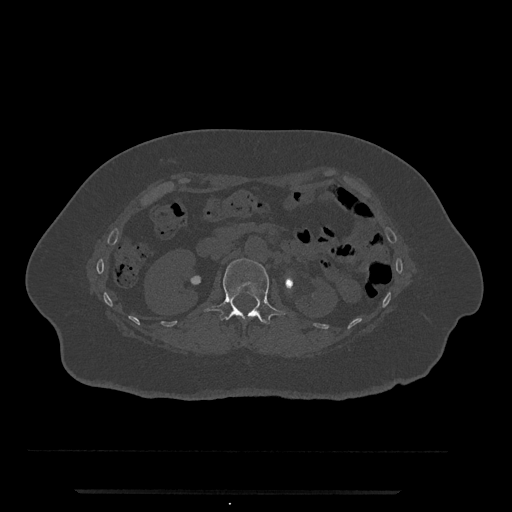
CT including the spine, one axial slice; position 106 of 797 along the scan axis; reconstruction kernel Br40s/3; 120 kVp; bone window (W 1800 / L 400 HU); 512 × 512 image matrix. Patient: female, 51 years. From the clinical record (not read from this slice): primary cancer: neuro; vertebrae with lytic lesions (as recorded): T8.
Outlined on this slice (semi-automatic segmentation, software-assisted and operator-edited):
- L1 vertebra: bounding box [x1, y1, x2, y2] px = [203, 259, 286, 325]